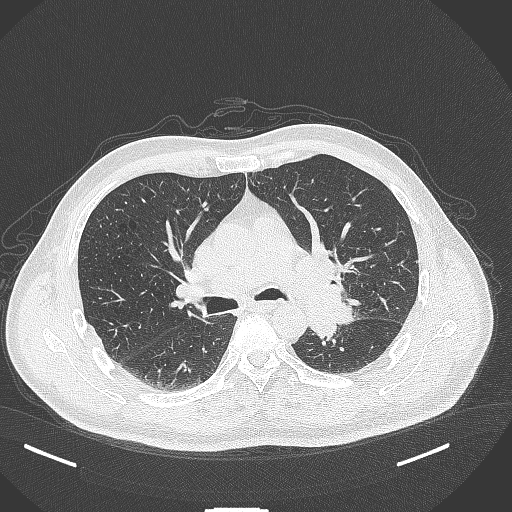
Chest CT, one axial slice; slice 254 of 429 in the series (ordered by position); reconstruction kernel B70f; lung window (W 1500 / L -600 HU); 1 mm slice thickness; 512 × 512 image matrix, field of view 400 × 400 mm. Male patient, age 55 years. Case-level facts recorded for this patient, not image findings: clinical TNM (as recorded): T3 N0 M1c; histopathological grade: G3.
Structures marked on this image (rectangle marked by the reading radiologist):
- lung tumour (recorded histology: adenocarcinoma): bounding box <307,289,361,343> (left, top, right, bottom; pixels)